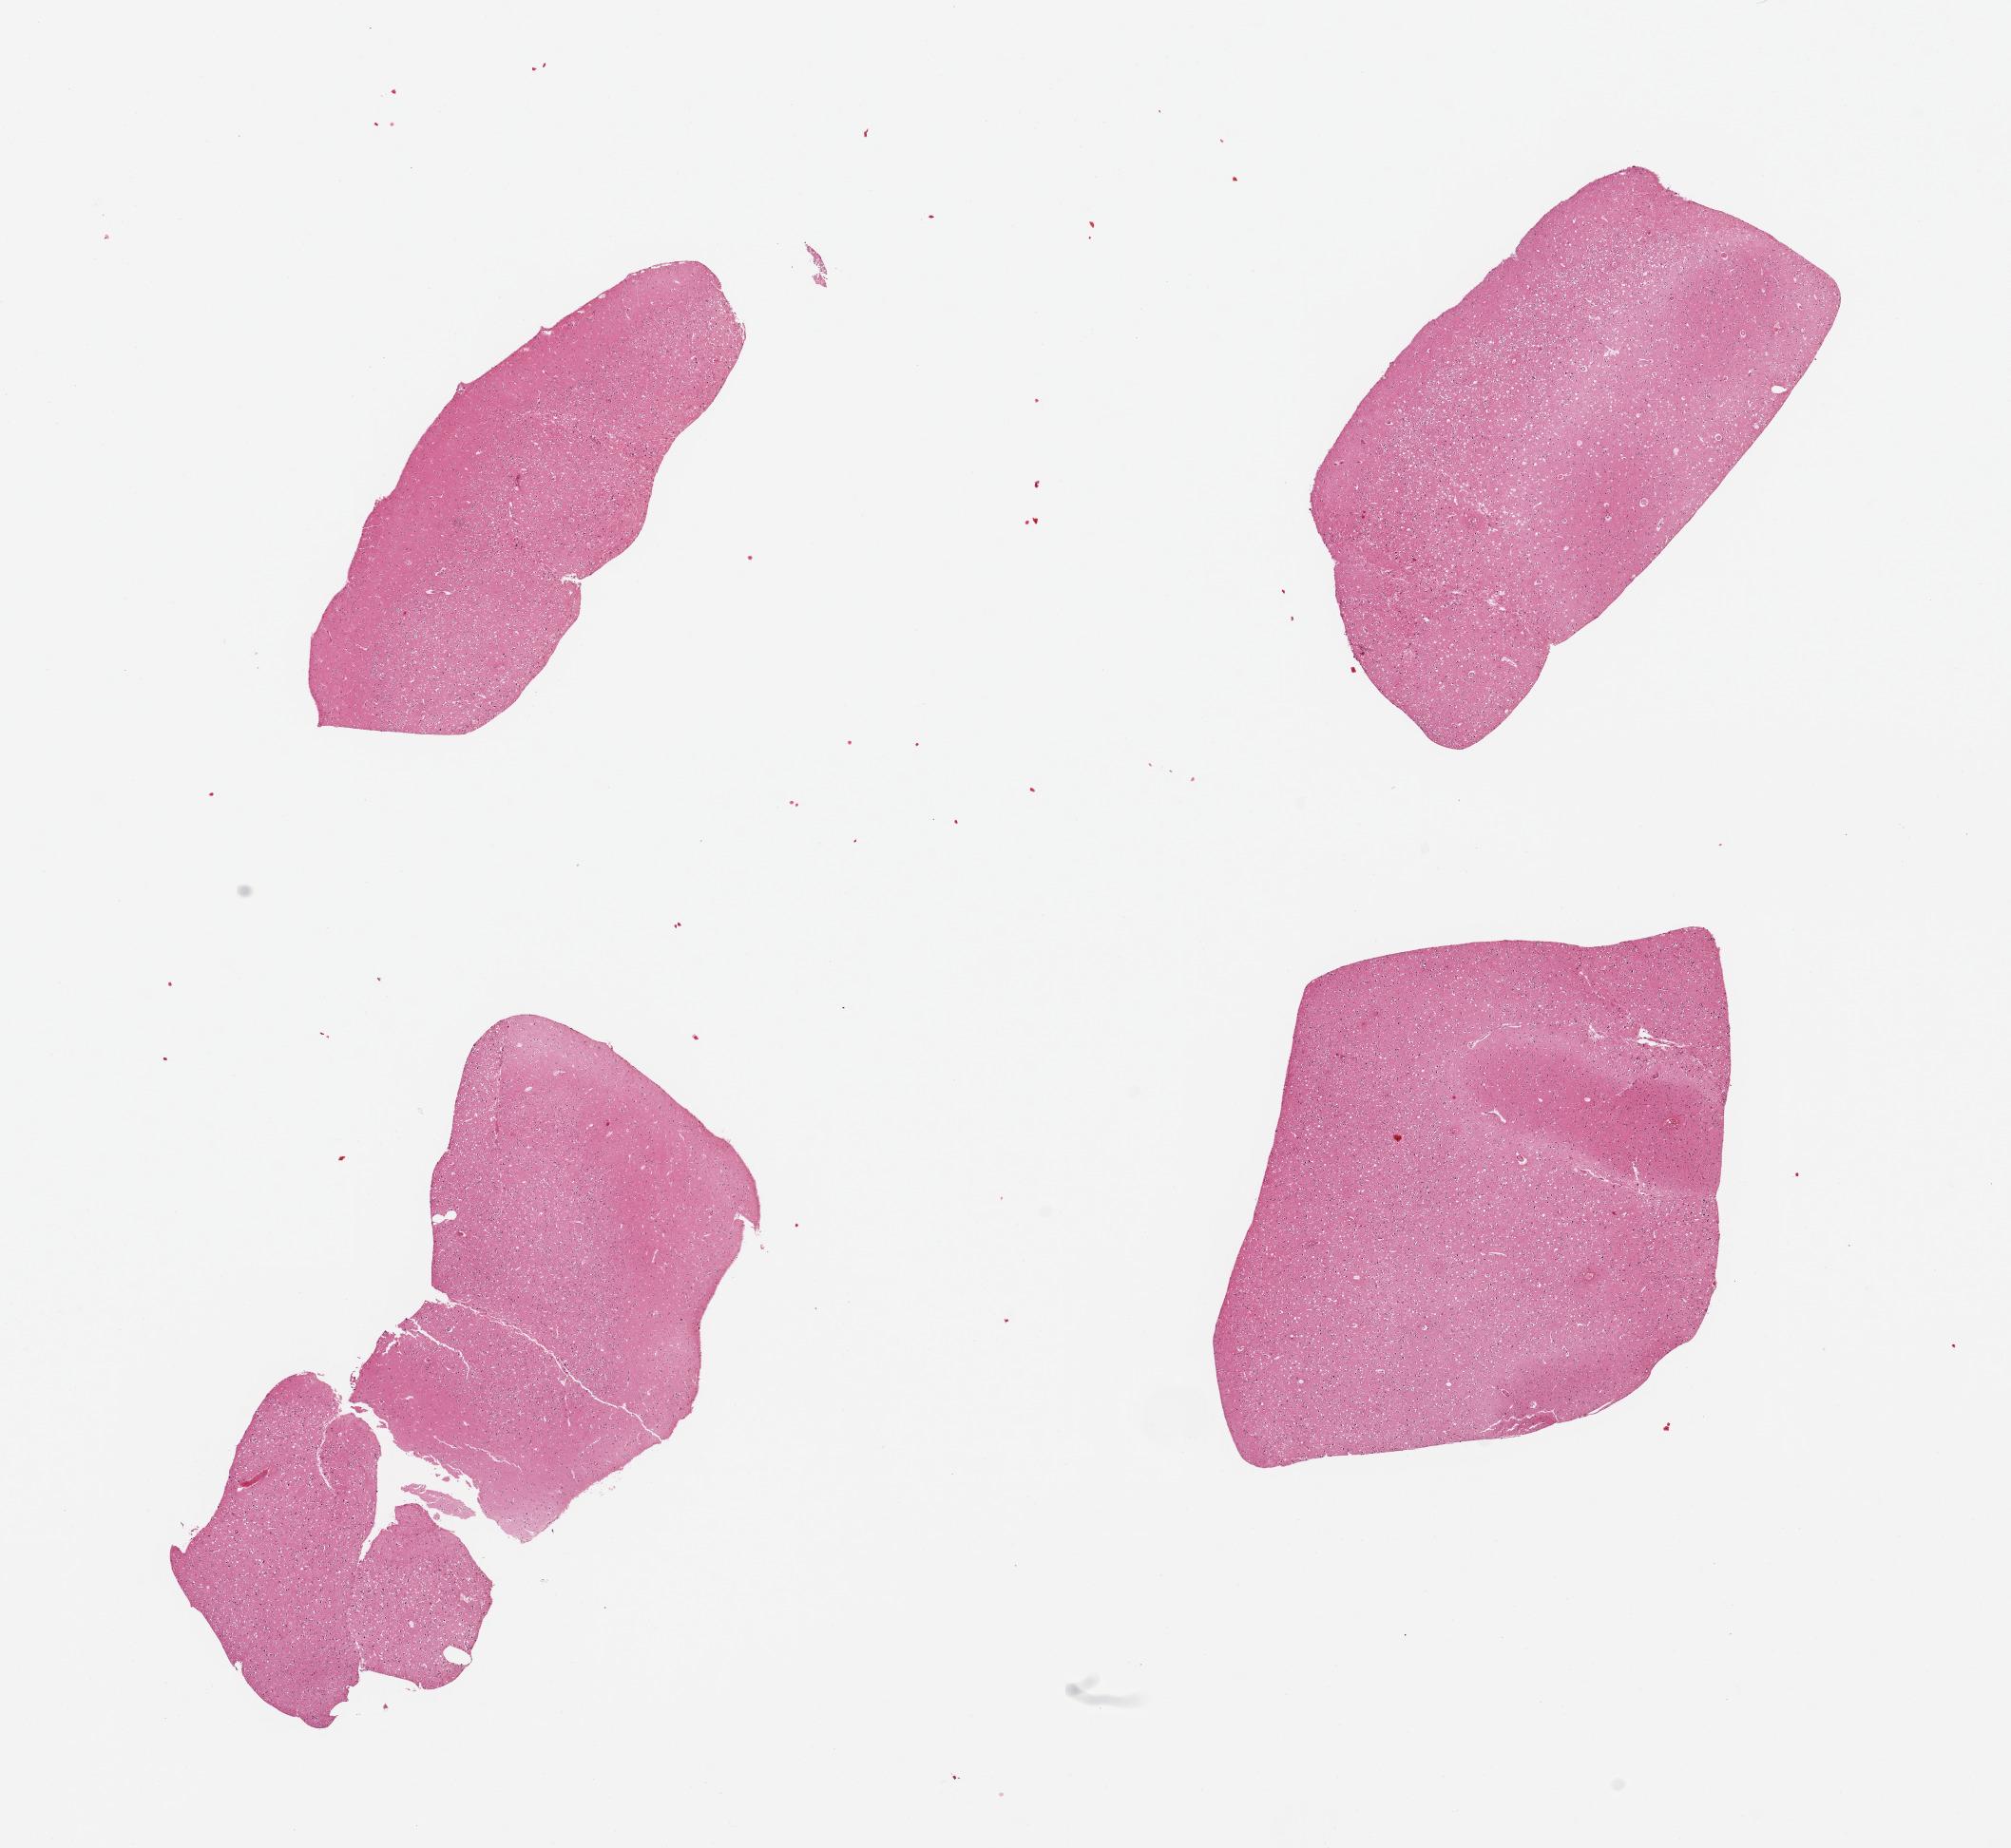
Hematoxylin and eosin (H&E) whole-slide image — shown as a low-resolution overview of the whole scanned area (about 16.7 x 15.4 mm, slide scanned at 20x), PAXgene-fixed paraffin-embedded (PFPE) section, target tissue: cerebral cortex, donor tissue sample. Donor sex: female.
• pathologist's review note for this sample: 4 pieces